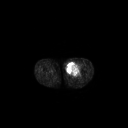
FDG PET of an extremity soft-tissue mass (from a PET/CT study), one axial slice. Position 235 of 267 along the scan axis. 3.27 mm slice thickness. 128 × 128 image matrix, field of view 700 × 700 mm. Male patient, age 63 years. Case-level facts recorded for this patient, not image findings: histological type: pleiomorphic liposarcoma; grade: high; site of the primary tumour: left thigh.
Annotated regions visible in this slice (expert contour drawn on MRI and transferred to this co-registered scan by the dataset authors):
- gross tumour volume including surrounding oedema: bounding box [x1, y1, x2, y2] px = [66, 61, 81, 76]
- gross tumour volume (mass): [66, 62, 80, 75]